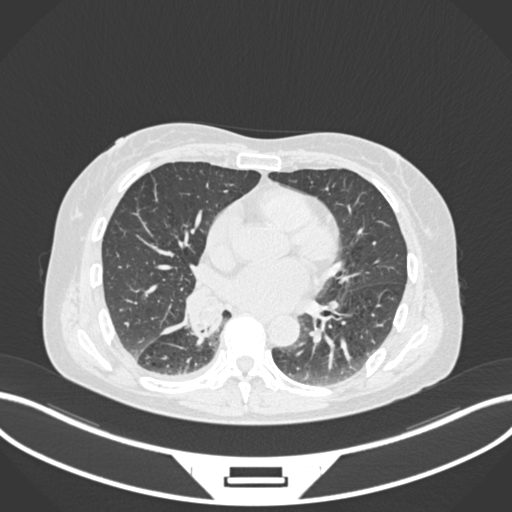
Chest CT, one axial slice. Slice 75 of 168 in the series (ordered by position). Reconstruction kernel B30f. Lung window (W 1500 / L -600 HU). 1 mm slice thickness. 512 × 512 image matrix, field of view 400 × 400 mm. Female patient, age 63 years. From the clinical record (not read from this slice): clinical TNM (as recorded): T1c N0 M0.
Outlined on this slice (rectangle marked by the reading radiologist):
- lung tumour (recorded histology: adenocarcinoma): box from (x=181, y=294) to (x=223, y=346) px